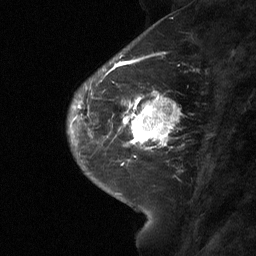
Breast MRI (dynamic contrast-enhanced), one sagittal slice. Position 21 of 64 along the scan axis. Dynamic contrast-enhanced study with each time point stored as its own series, time point 2 of 3 at this slice position (early post-contrast, ordered by acquisition time). 1.5 T. TE 4.8 ms, TR 27 ms. 2 mm slice thickness. 256 × 256 image matrix, field of view 180 × 180 mm. Patient: female, 42 years. Case-level facts recorded for this patient, not image findings: setting: breast cancer imaged before/during neoadjuvant chemotherapy; receptor status: triple-negative.
Annotated regions visible in this slice (semi-automatically segmented with operator editing):
- analysis volume of interest (the breast-tissue region the enhancement analysis was run in; not a lesion): bounding box (x1, y1, x2, y2) in pixels: (115, 85, 179, 160)
- tumour enhancement mask (voxels above the 90 % enhancement threshold inside the analysis volume of interest): (121, 95, 174, 160)